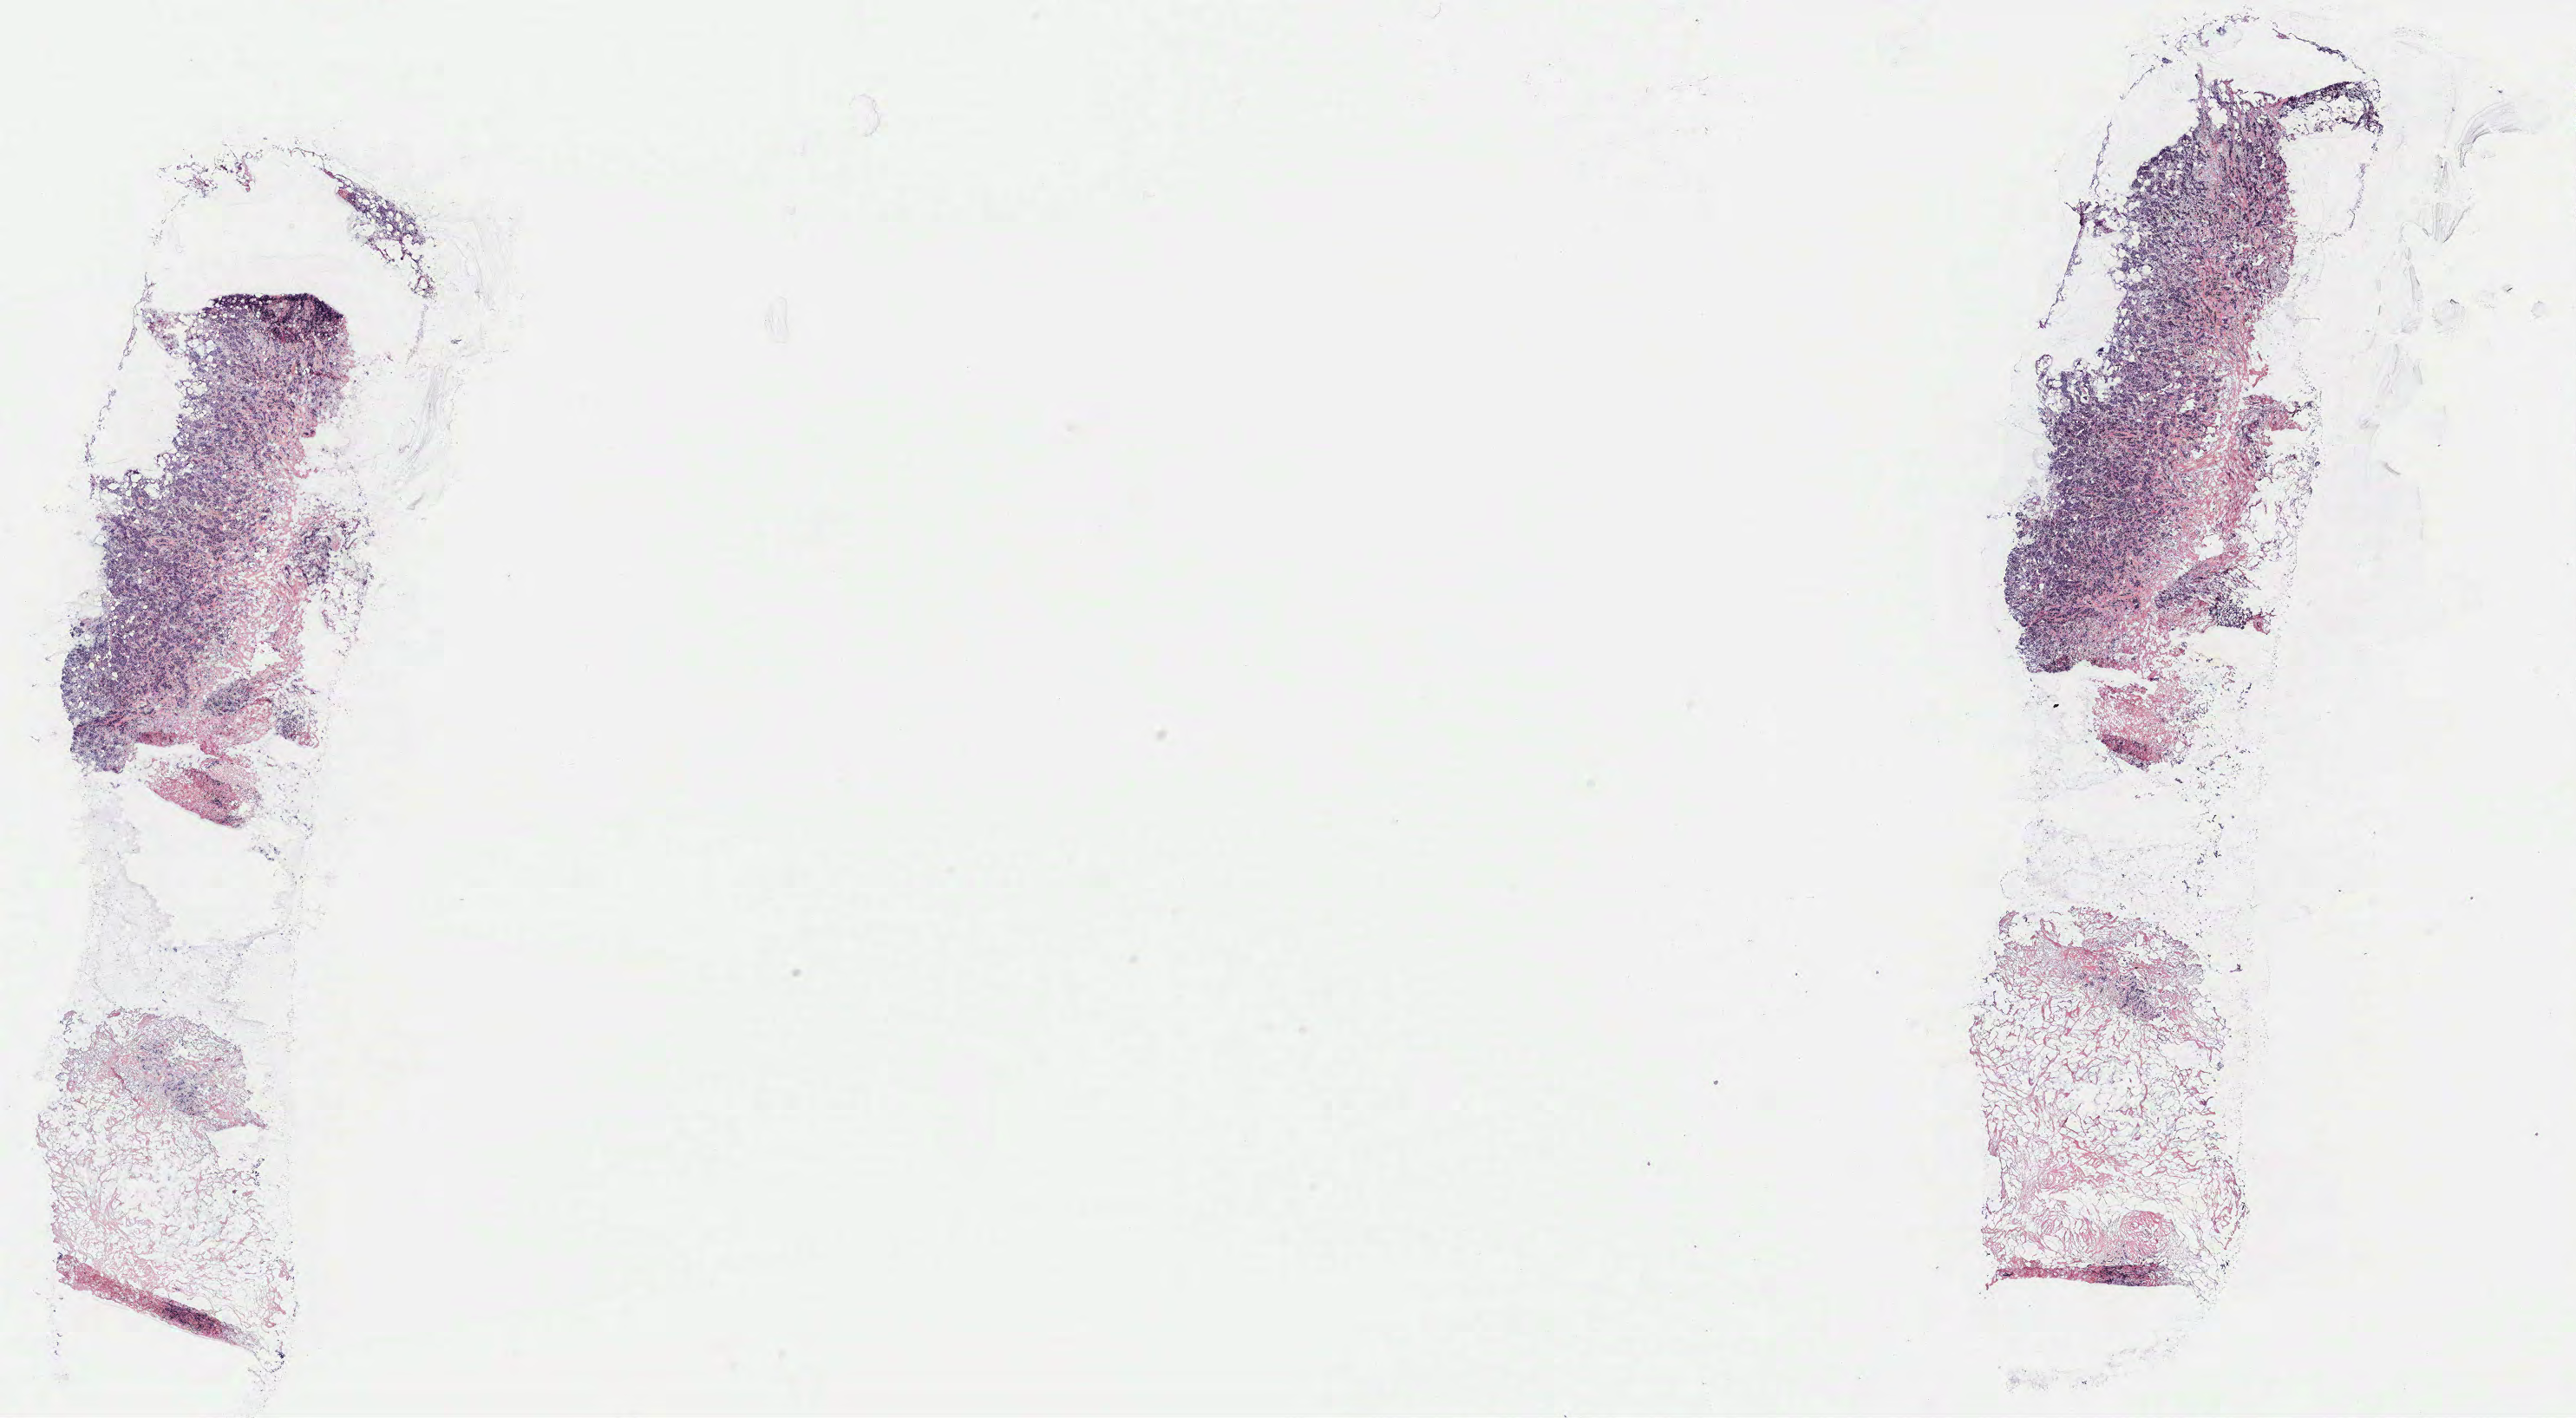
Whole-slide histology image, H&E — shown as a low-resolution overview of the whole scanned area (about 23.8 x 13.1 mm, slide scanned at 40x); breast, tissue type not recorded. 34-year-old female patient.
Patient diagnosis: Infiltrating duct carcinoma, NOS.